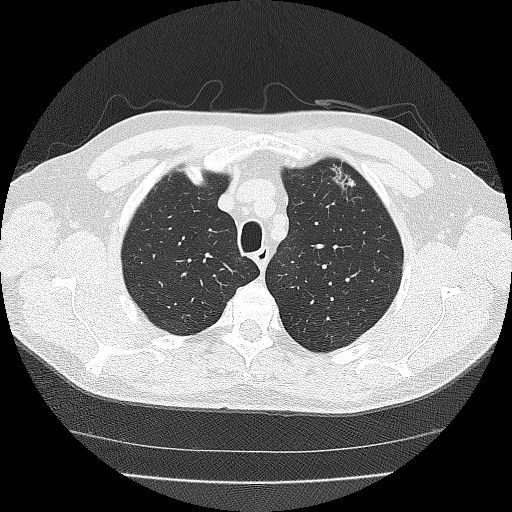
Low-dose screening chest CT, axial slice. Third annual screen. Lung window (W 1500 / L -600 HU). 2 mm slice thickness. 512 × 512 image matrix. Male participant, aged 56 years at enrolment. Former smoker at enrolment.
Expert-annotated lung lesion, bounding box (x1, y1, x2, y2) in pixels: (320, 155, 361, 196). Screening reader's record for this exam (one nodule recorded; not confirmed to be the boxed lesion): non-calcified nodule or mass ≥4 mm, left upper lobe, 18 × 10 mm, spiculated (stellate) margins, soft tissue attenuation, pre-existing on the prior screen: yes; interval growth: yes.